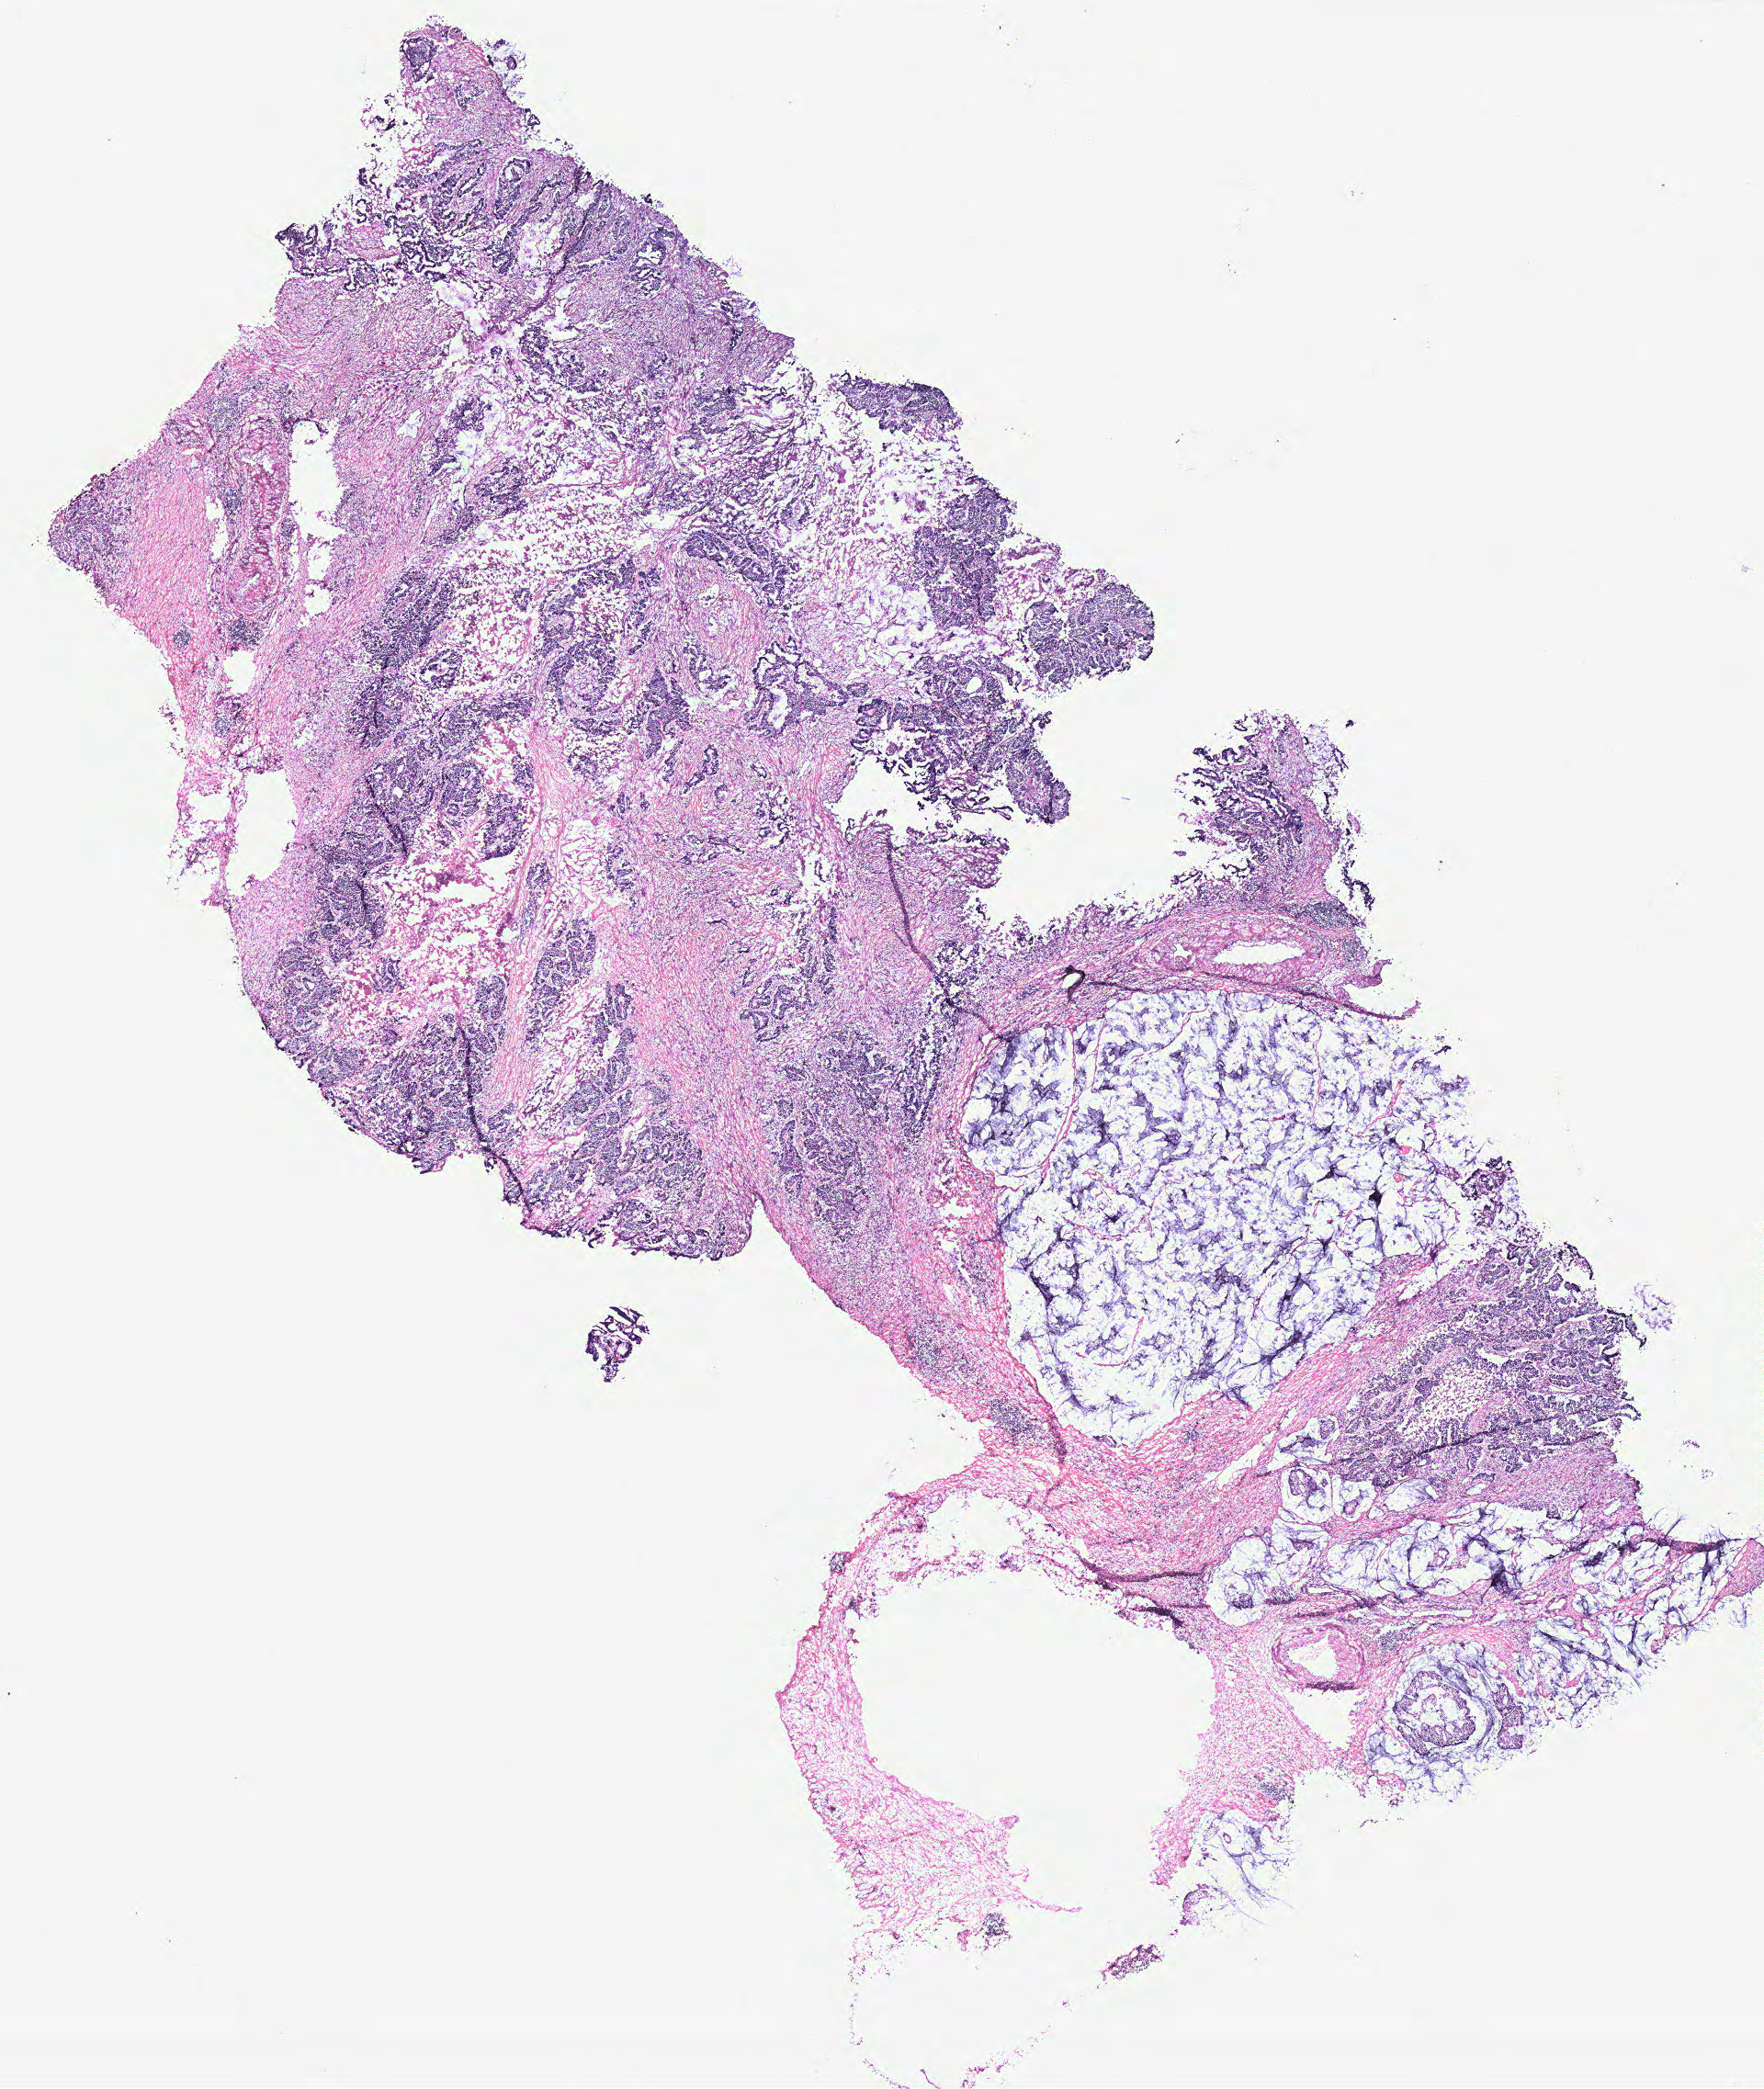
H&E-stained whole-slide image, shown as a low-resolution overview of the whole scanned area (about 15.4 x 18.2 mm, slide scanned at 40x), colon, tumour tissue. Male, 35 y/o.
AJCC pathologic stage: IIIB. Primary tumour site (as recorded): colon. Diagnosis: Adenocarcinoma, NOS.